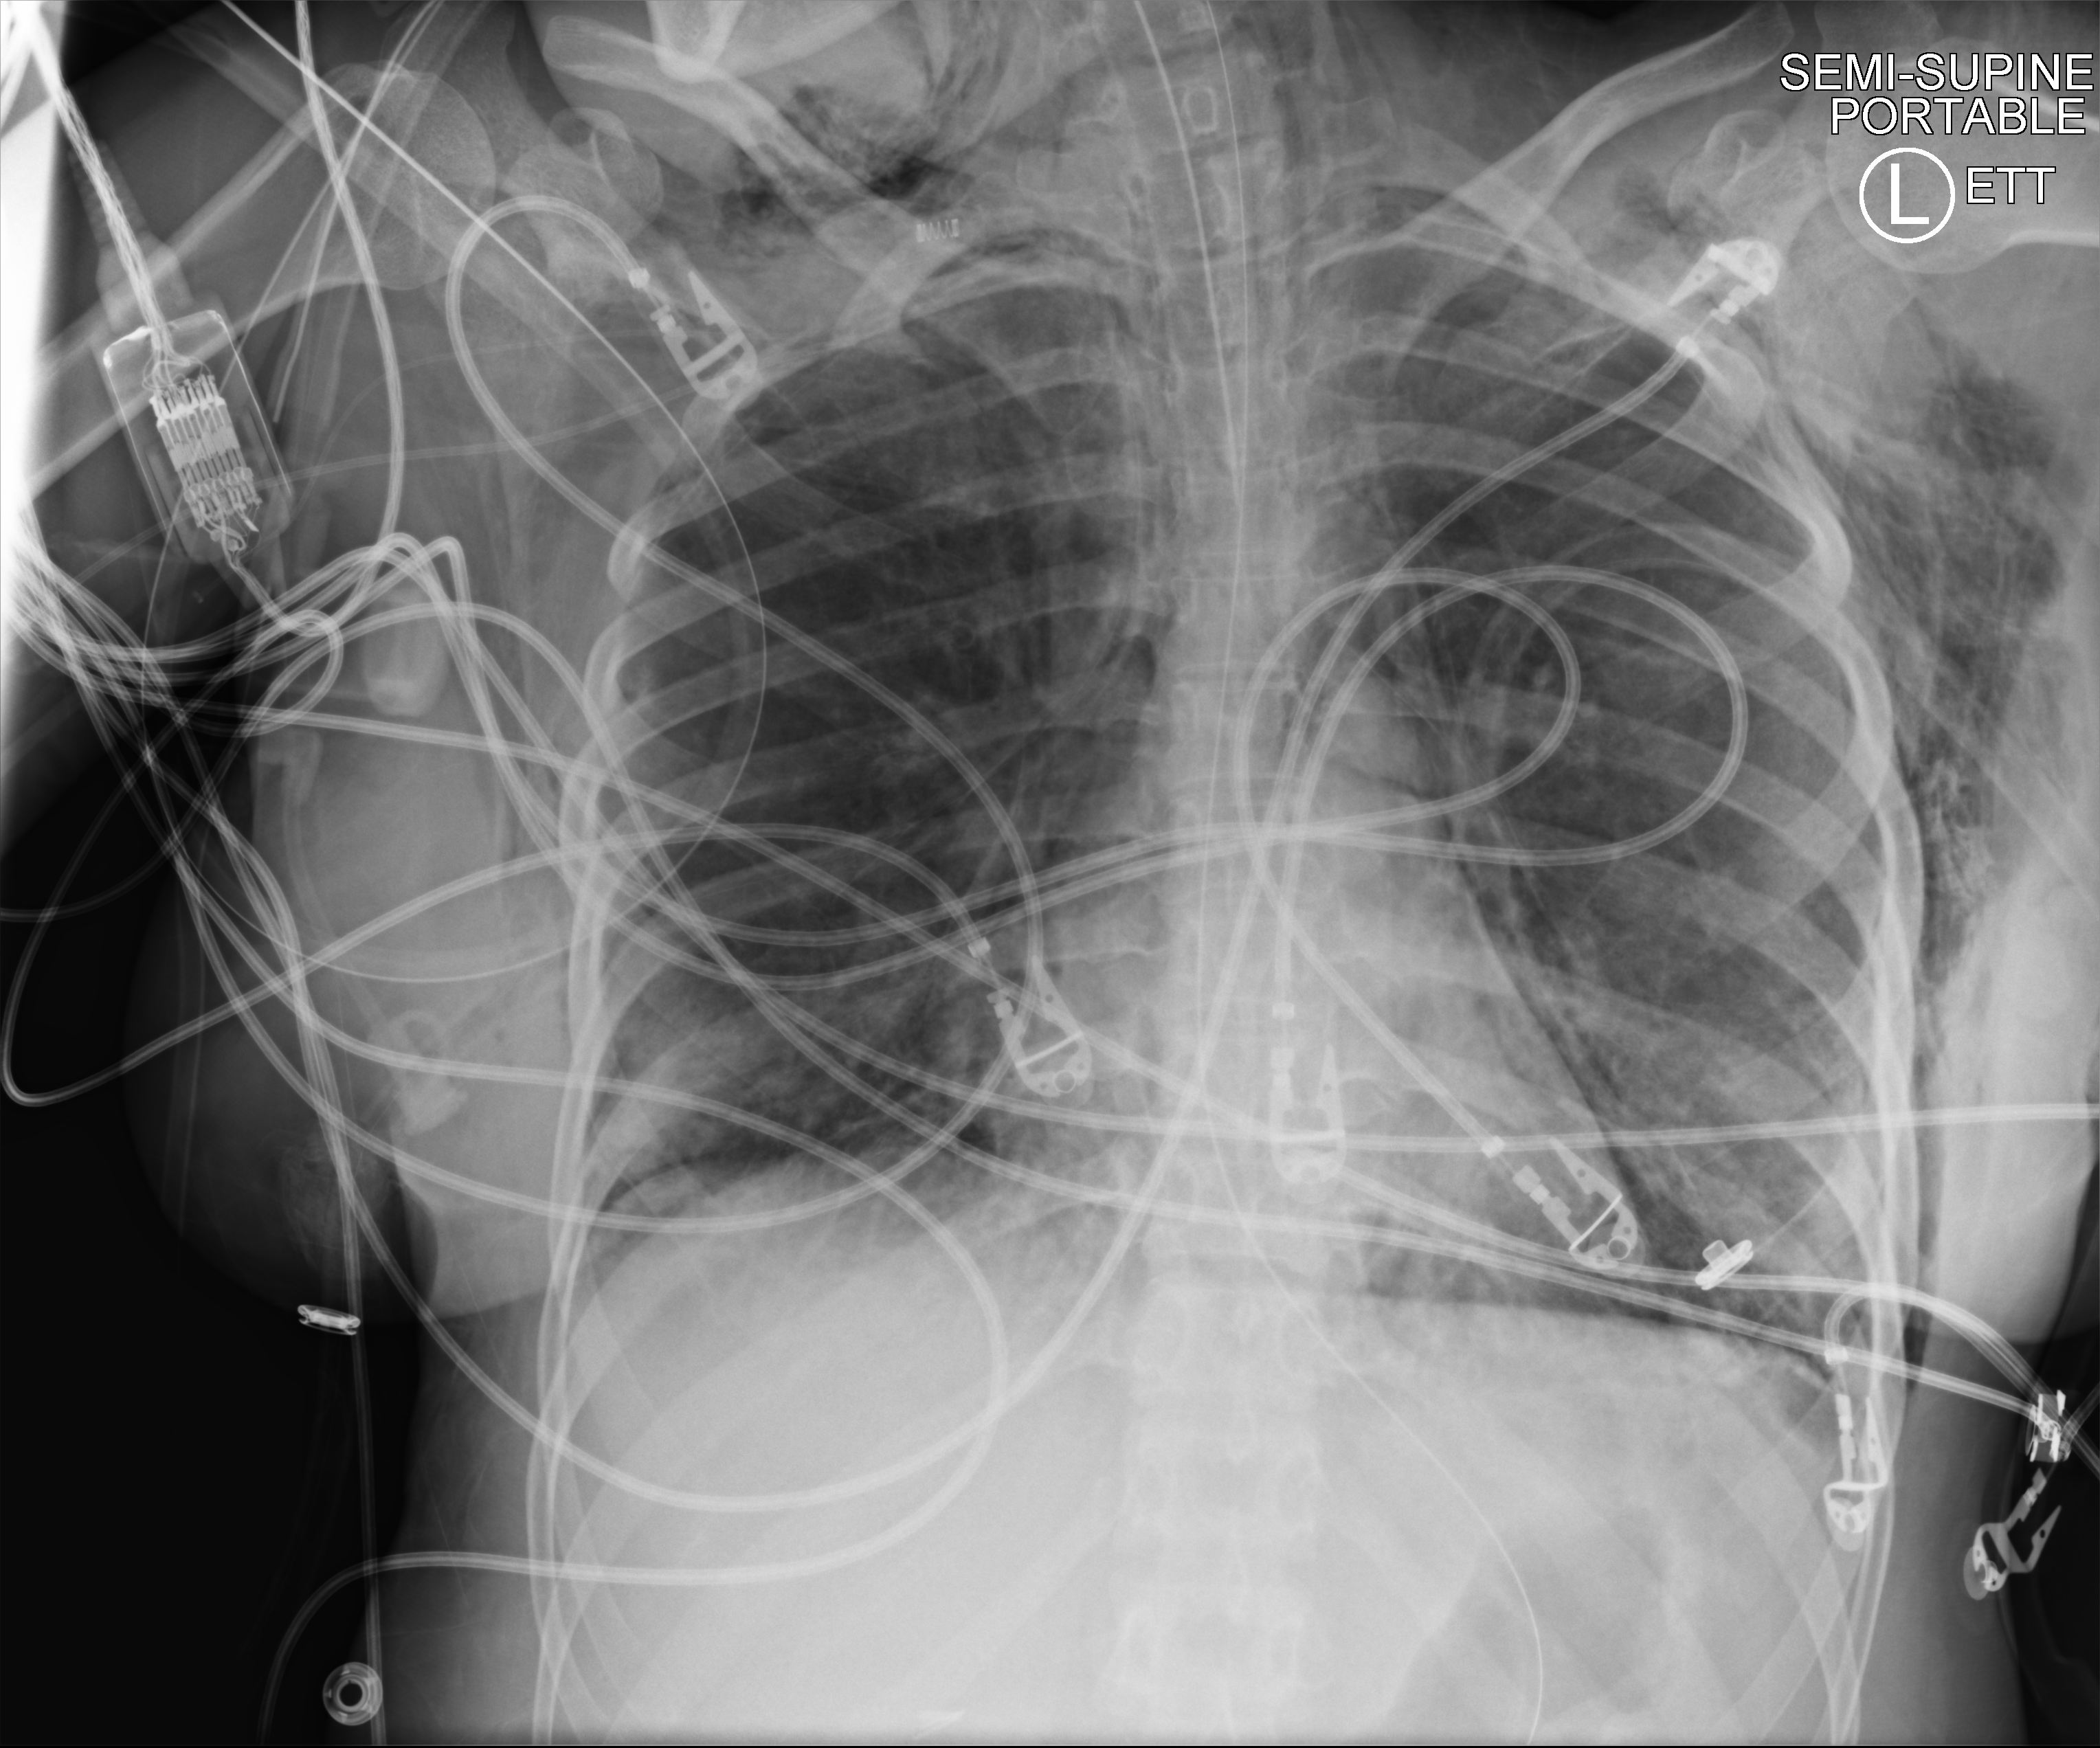
Portable chest radiograph; anteroposterior (AP) projection. Adult patient hospitalised with COVID-19, age 18–59 years.
From the hospital-stay record, not from the radiograph (when in the stay this image was taken is not recorded):
- admitted to intensive care during this hospital stay: yes
- mechanically ventilated during this hospital stay: yes